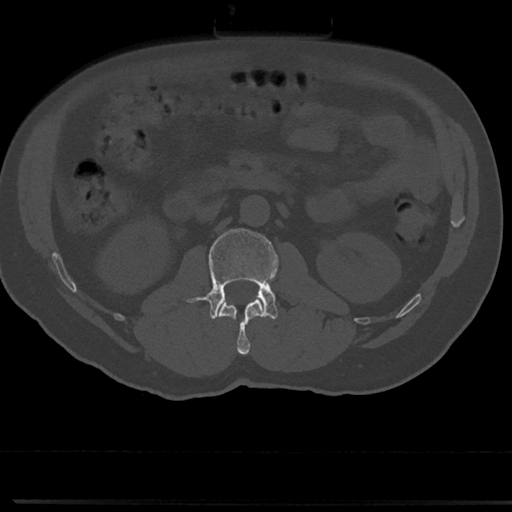
CT including the spine, one axial slice; slice 37 of 817 in the series (ordered by position); 120 kVp; bone window (W 1800 / L 400 HU); 0.5 mm slice thickness; 512 × 512 image matrix, field of view 355 × 355 mm. Male patient, age 61 years. From the clinical record (not read from this slice): primary cancer: prostate.
Annotated regions visible in this slice (semi-automatically segmented with operator editing):
- L1 vertebra: bounding box [x1, y1, x2, y2] px = [219, 299, 263, 355]
- L2 vertebra: [191, 228, 278, 318]